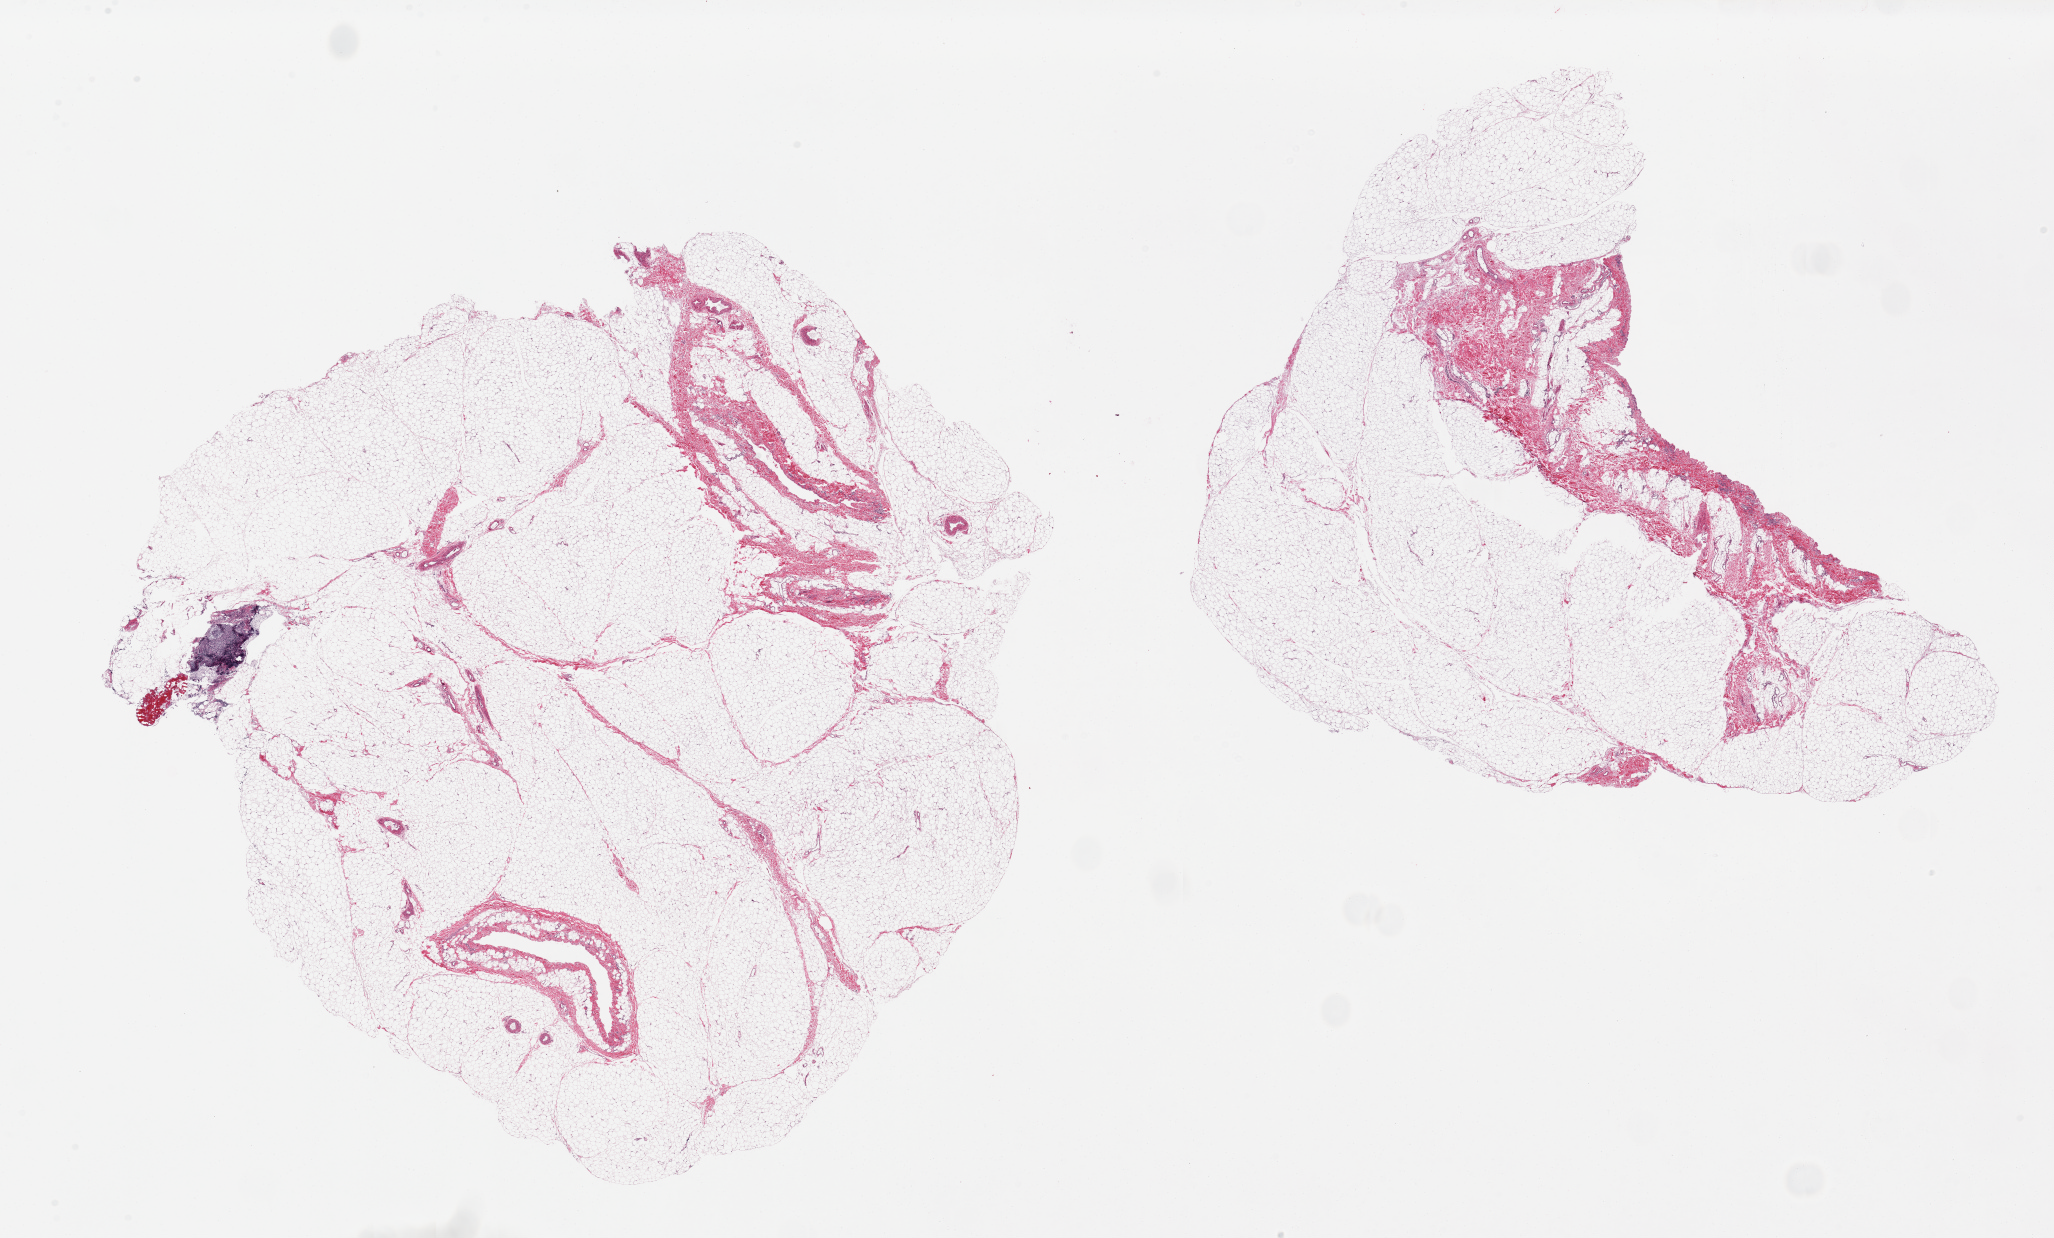
Whole-slide image, hematoxylin and eosin (H&E) stain, brightfield, a low-resolution overview of the entire scanned area, about 32.5 x 19.6 mm. PAXgene-fixed, paraffin-embedded tissue. Target tissue: omentum. Tissue donor sample.
Pathologist's review note for this sample: 2 pieces. 14.5x14 & 13x11mm. 1 with 0.7mm lymphoid nodule. 1 with 25% fibrous stroma.